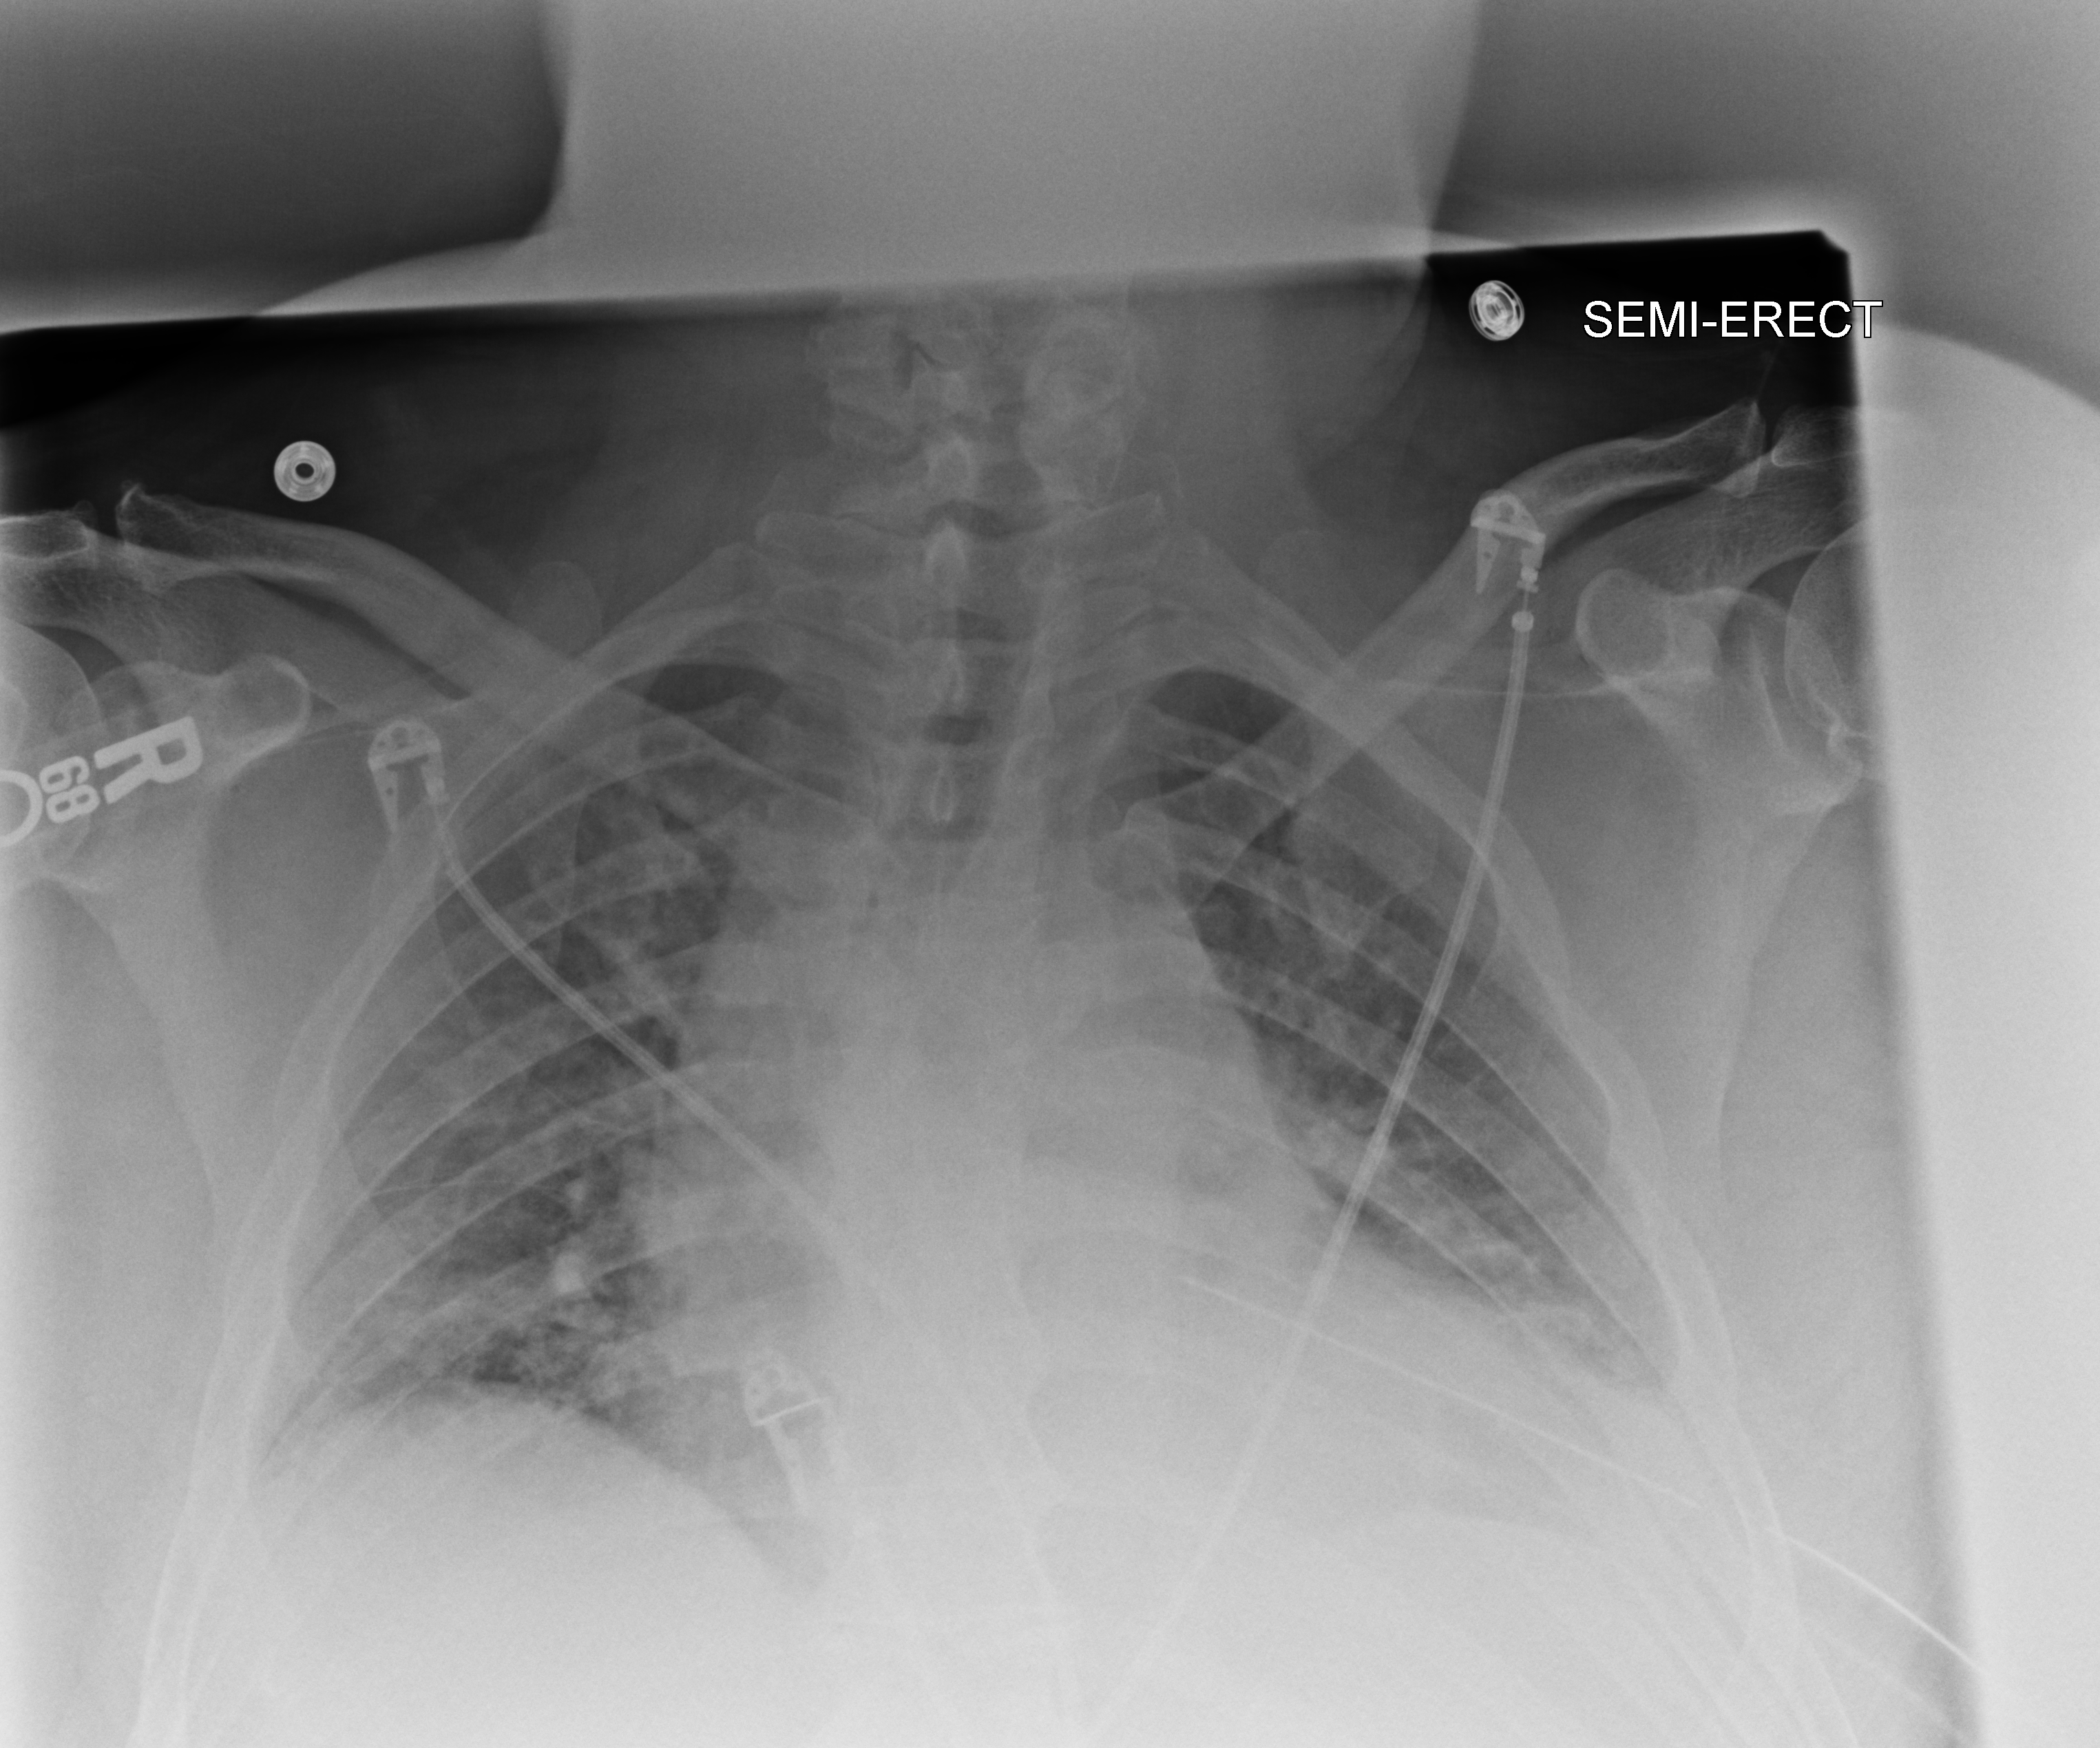
Chest X-ray (portable); anteroposterior (AP) projection. Male patient hospitalised with COVID-19, age 18–59 years.
Admission-level facts for this patient (not findings on this image; timing relative to this image not recorded): length of hospital stay: 10 days; mechanically ventilated during this hospital stay: no.